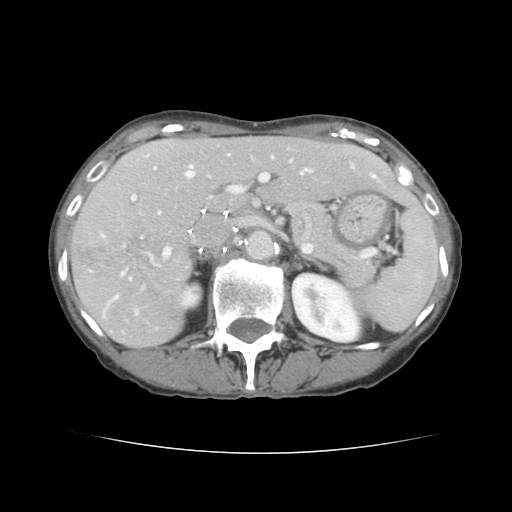
Contrast-enhanced abdominal CT, one axial slice; slice 85 of 136 in the series (ordered by position); intravenous contrast given; soft-tissue window (W 400 / L 40 HU); 2.5 mm slice thickness; 512 × 512 image matrix, field of view 319 × 319 mm. Female patient, age 77 years. From the clinical record (not read from this slice): diagnosis: colorectal cancer liver metastases, imaged before liver resection; multiple liver metastases: yes; largest metastasis: 3 cm; disease in both lobes: no.
Structures marked on this image (expert manual segmentation):
- hepatic veins: bounding box <186,155,376,178> (left, top, right, bottom; pixels)
- liver: <72,137,418,347>
- planned liver remnant (the part of the liver to remain after resection): <153,137,417,211>
- portal vein (with intrahepatic branches): <102,155,292,313>
- liver metastasis: <127,235,150,261>